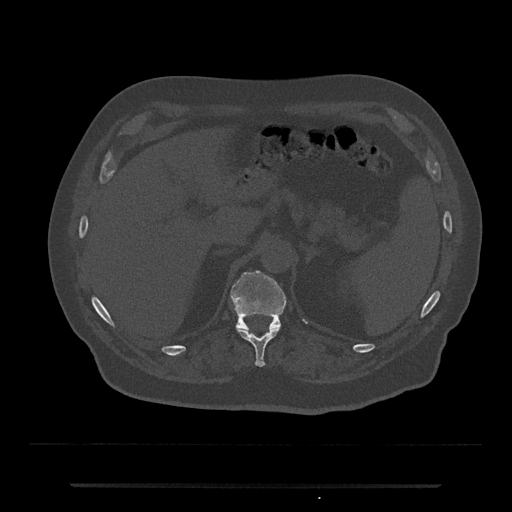
CT including the spine, one axial slice; position 624 of 797 along the scan axis; reconstruction kernel Br40s/3; bone window (W 1800 / L 400 HU); 0.5 mm slice thickness; 512 × 512 image matrix, field of view 434 × 434 mm. Male patient, age 80 years. Case-level facts recorded for this patient, not image findings: primary cancer: prostate; vertebrae with lytic lesions (as recorded): L1, T11.
Outlined on this slice (semi-automatically segmented with operator editing):
- T11 vertebra: box from (x=237, y=328) to (x=280, y=367) px
- T12 vertebra: (x=230, y=270)–(x=287, y=331)